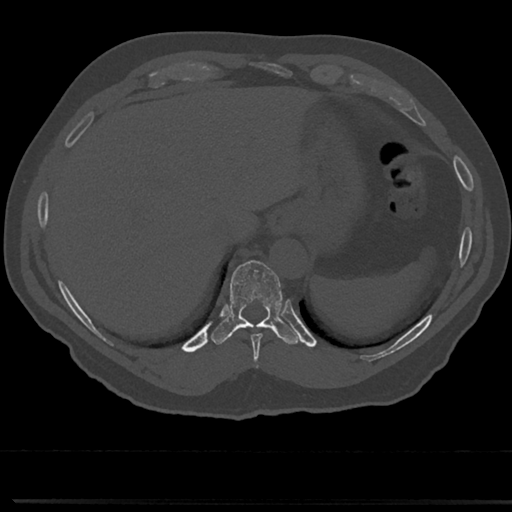
CT including the spine, one axial slice; position 268 of 817 along the scan axis; reconstruction kernel Br40s/3; bone window (W 1800 / L 400 HU); 512 × 512 image matrix, field of view 355 × 355 mm. Male patient, age 61 years. From the clinical record (not read from this slice): primary cancer: prostate.
Annotated regions visible in this slice (semi-automatically segmented with operator editing):
- T10 vertebra: bounding box (x1, y1, x2, y2) in pixels: (229, 261, 283, 325)
- T9 vertebra: (238, 322, 278, 354)